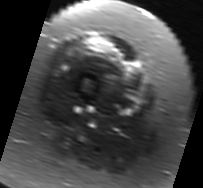
MRI of an extremity soft-tissue mass, one axial slice; T2-weighted fat-saturated; MR volume resampled by the dataset authors to the PET/CT grid (not the native acquisition matrix); 3.27 mm slice thickness; 203 × 188 image matrix, field of view 198 × 184 mm. Female patient. Case-level facts recorded for this patient, not image findings: histological type: malignant solitary fibrous tumor; grade: intermediate; site of the primary tumour: right thigh.
Annotated regions visible in this slice (expert contour drawn on MRI and transferred to this co-registered scan by the dataset authors):
- gross tumour volume including surrounding oedema: bounding box <79,35,134,75> (left, top, right, bottom; pixels)